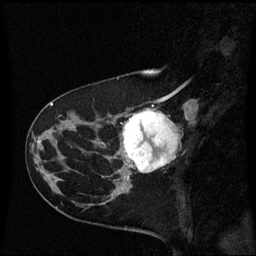
Breast MRI (dynamic contrast-enhanced), one sagittal slice; slice 22 of 60 in the series (ordered by position); dynamic contrast-enhanced series, image 2 of 3 at this slice position (ordered by acquisition); 1.5 T; TE 4.2 ms, TR 8.4 ms; 256 × 256 image matrix. Female patient, age 41 years. Case-level facts recorded for this patient, not image findings: setting: breast cancer imaged before/during neoadjuvant chemotherapy; receptor status: triple-negative.
Annotated regions visible in this slice (semi-automatic segmentation, software-assisted and operator-edited):
- analysis volume of interest (the breast-tissue region the enhancement analysis was run in; not a lesion): bounding box <116,108,178,177> (left, top, right, bottom; pixels)
- tumour enhancement mask (voxels above the 70 % enhancement threshold inside the analysis volume of interest): <122,110,178,173>